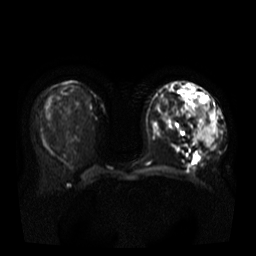
Breast MRI, one axial slice; slice 18 of 37 in the series (ordered by position); diffusion-weighted series; image 2 of 4 stored at this slice position (different b-values; order by instance number); 3 T; 256 × 256 image matrix, field of view 380 × 380 mm. Female patient.
Outlined on this slice (outlined manually by an expert reader):
- tumour on diffusion-weighted imaging: bounding box <197,105,215,146> (left, top, right, bottom; pixels)